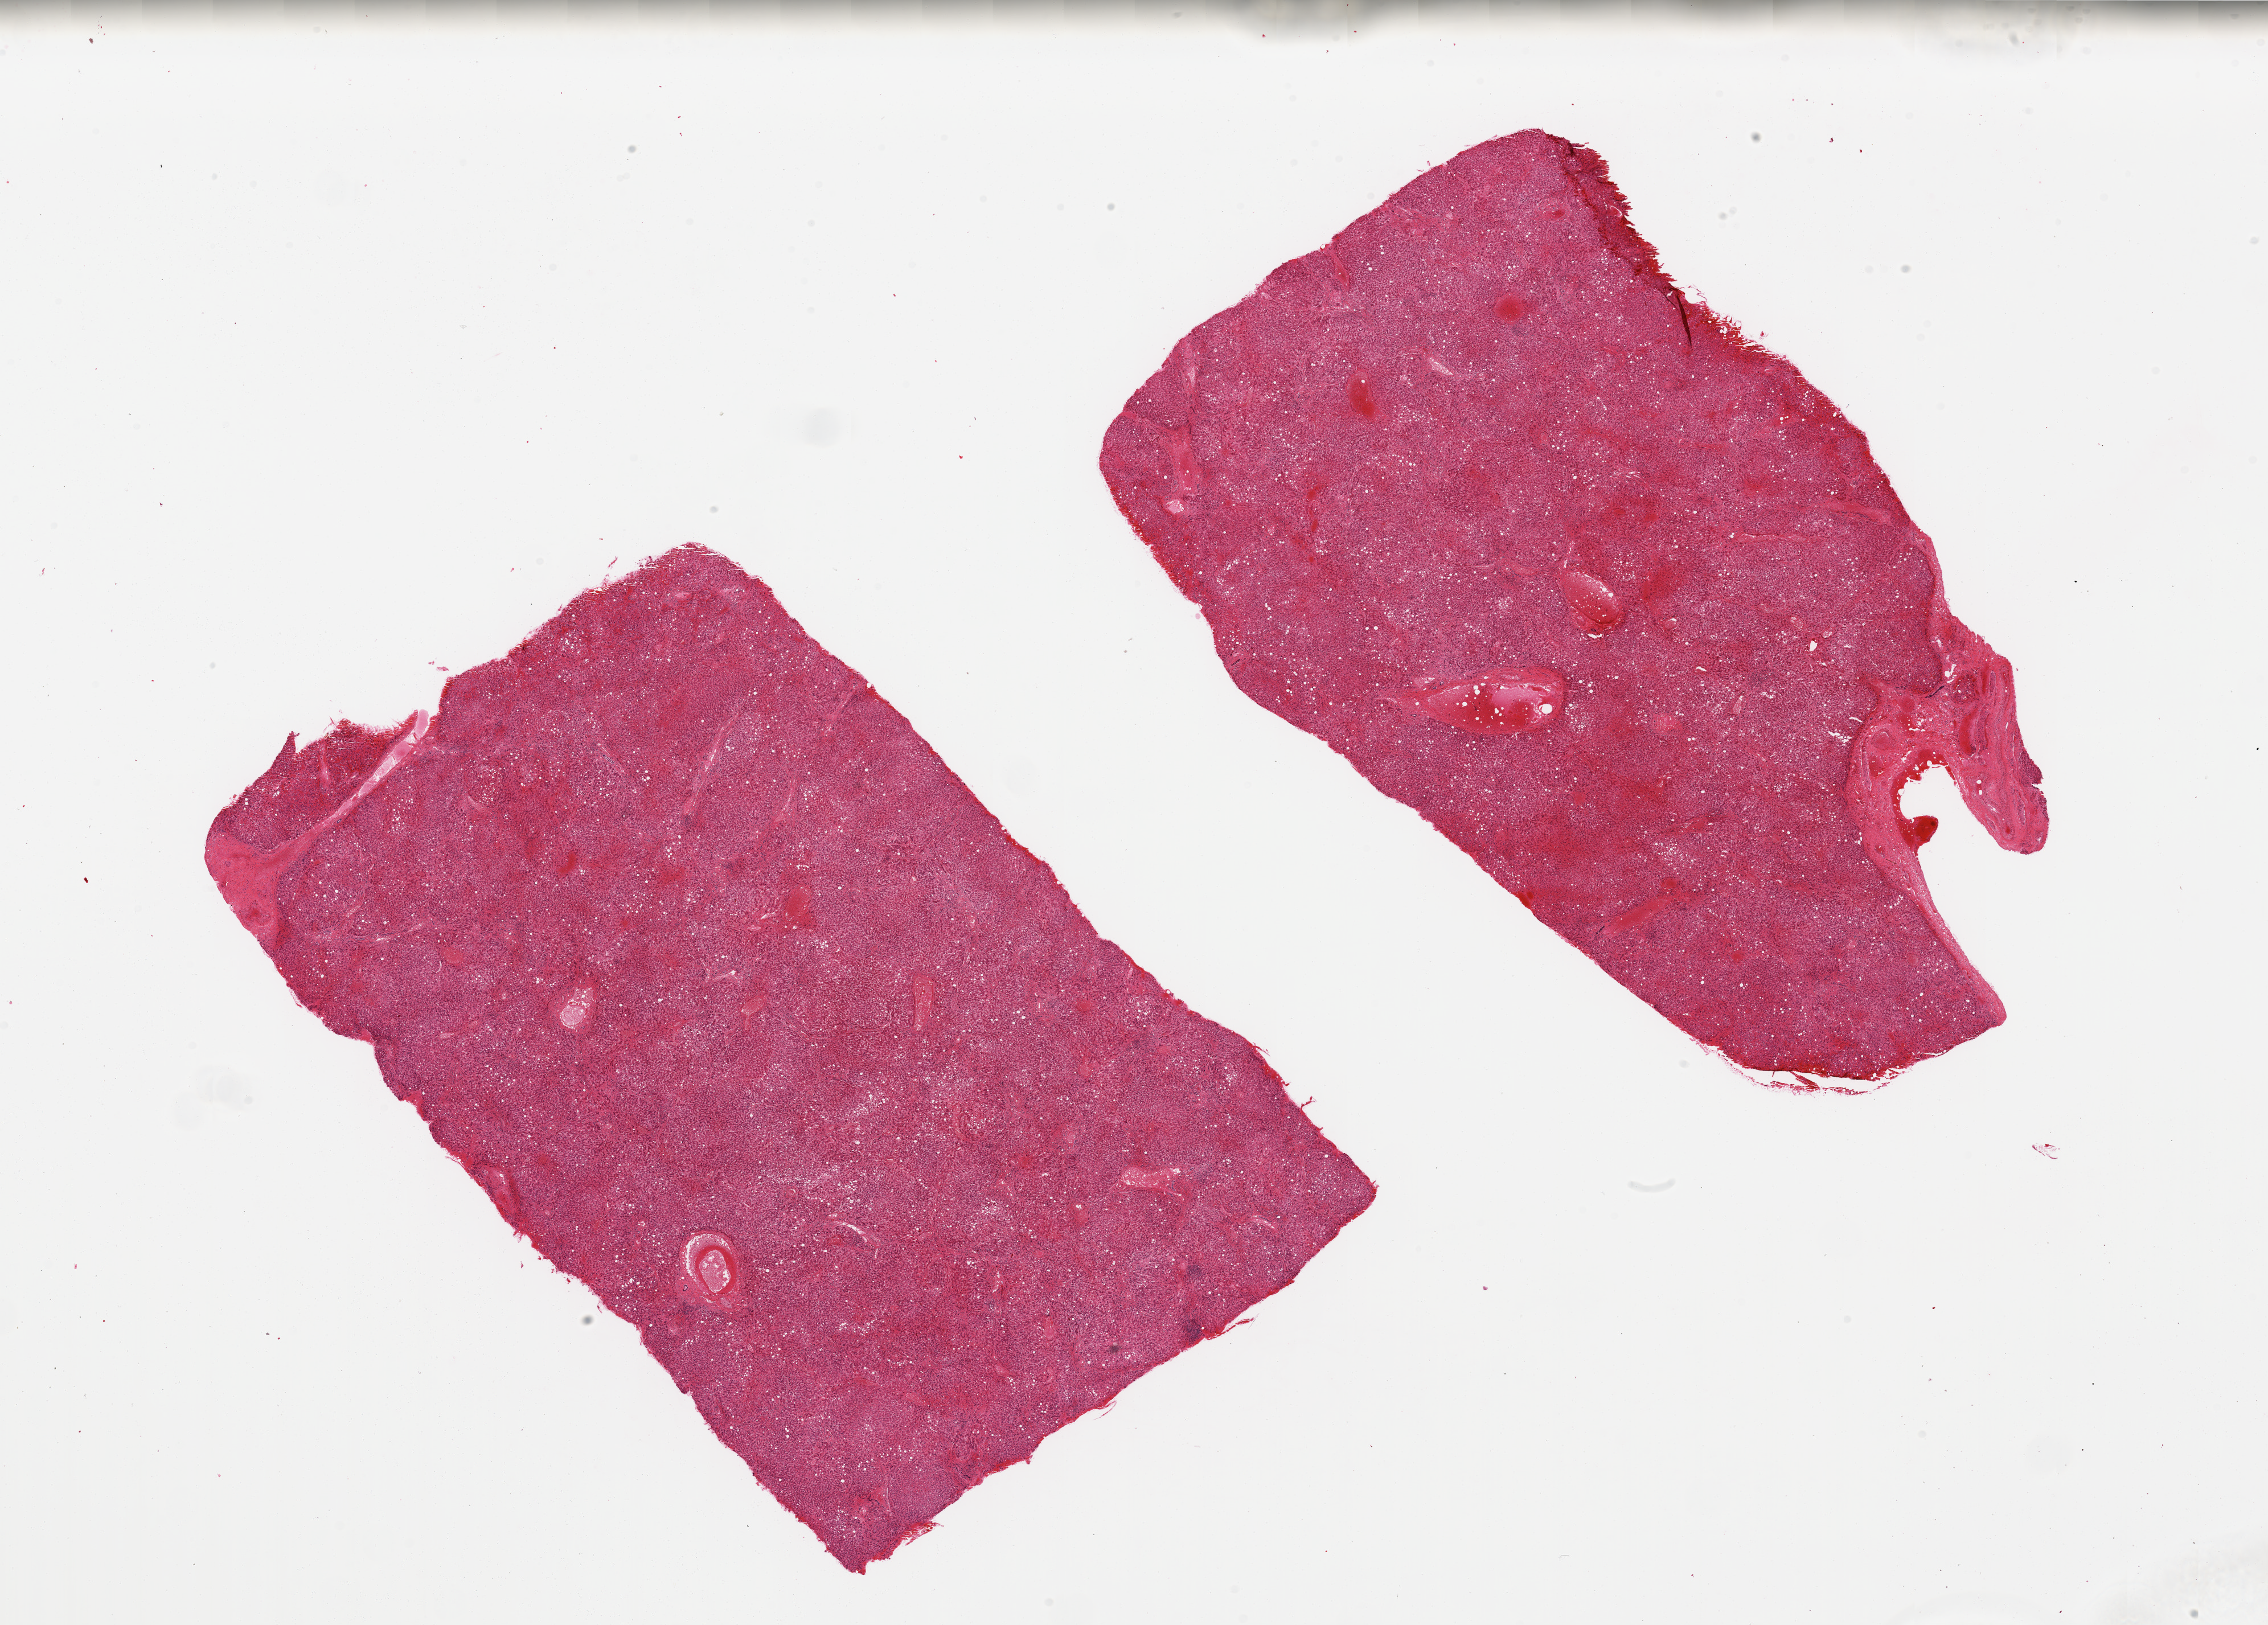
Digitized haematoxylin and eosin-stained section, brightfield, low-resolution overview of the scanned area, about 31.5 x 22.6 mm (from a 20x scan), PAXgene-fixed, paraffin-embedded tissue, target tissue: liver, tissue donor sample. Donor: male.
- pathologist's review note for this sample: 2 pieces moderate macro and microvesicular steatosis, moderate congestion, early bridging fibrosis